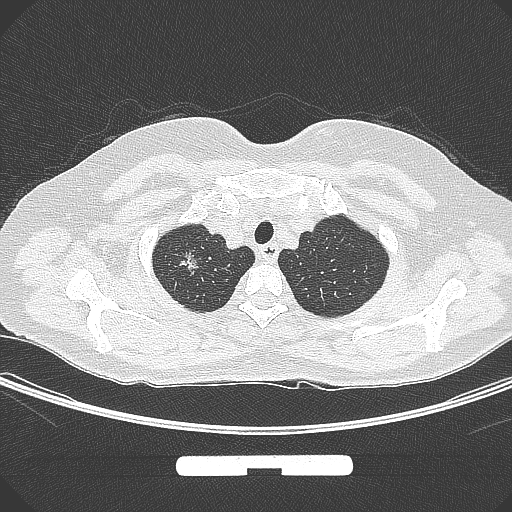
Chest CT, one axial slice; slice 260 of 295 in the series (ordered by position); 120 kVp; lung window (W 1500 / L -600 HU); 1 mm slice thickness; 512 × 512 image matrix, field of view 369 × 369 mm. Patient: female, 58 years. Case-level facts recorded for this patient, not image findings: clinical TNM (as recorded): T1b N0 M0.
Outlined on this slice (bounding box drawn by a radiologist):
- lung tumour (recorded histology: adenocarcinoma): bounding box (x1, y1, x2, y2) in pixels: (175, 243, 207, 282)